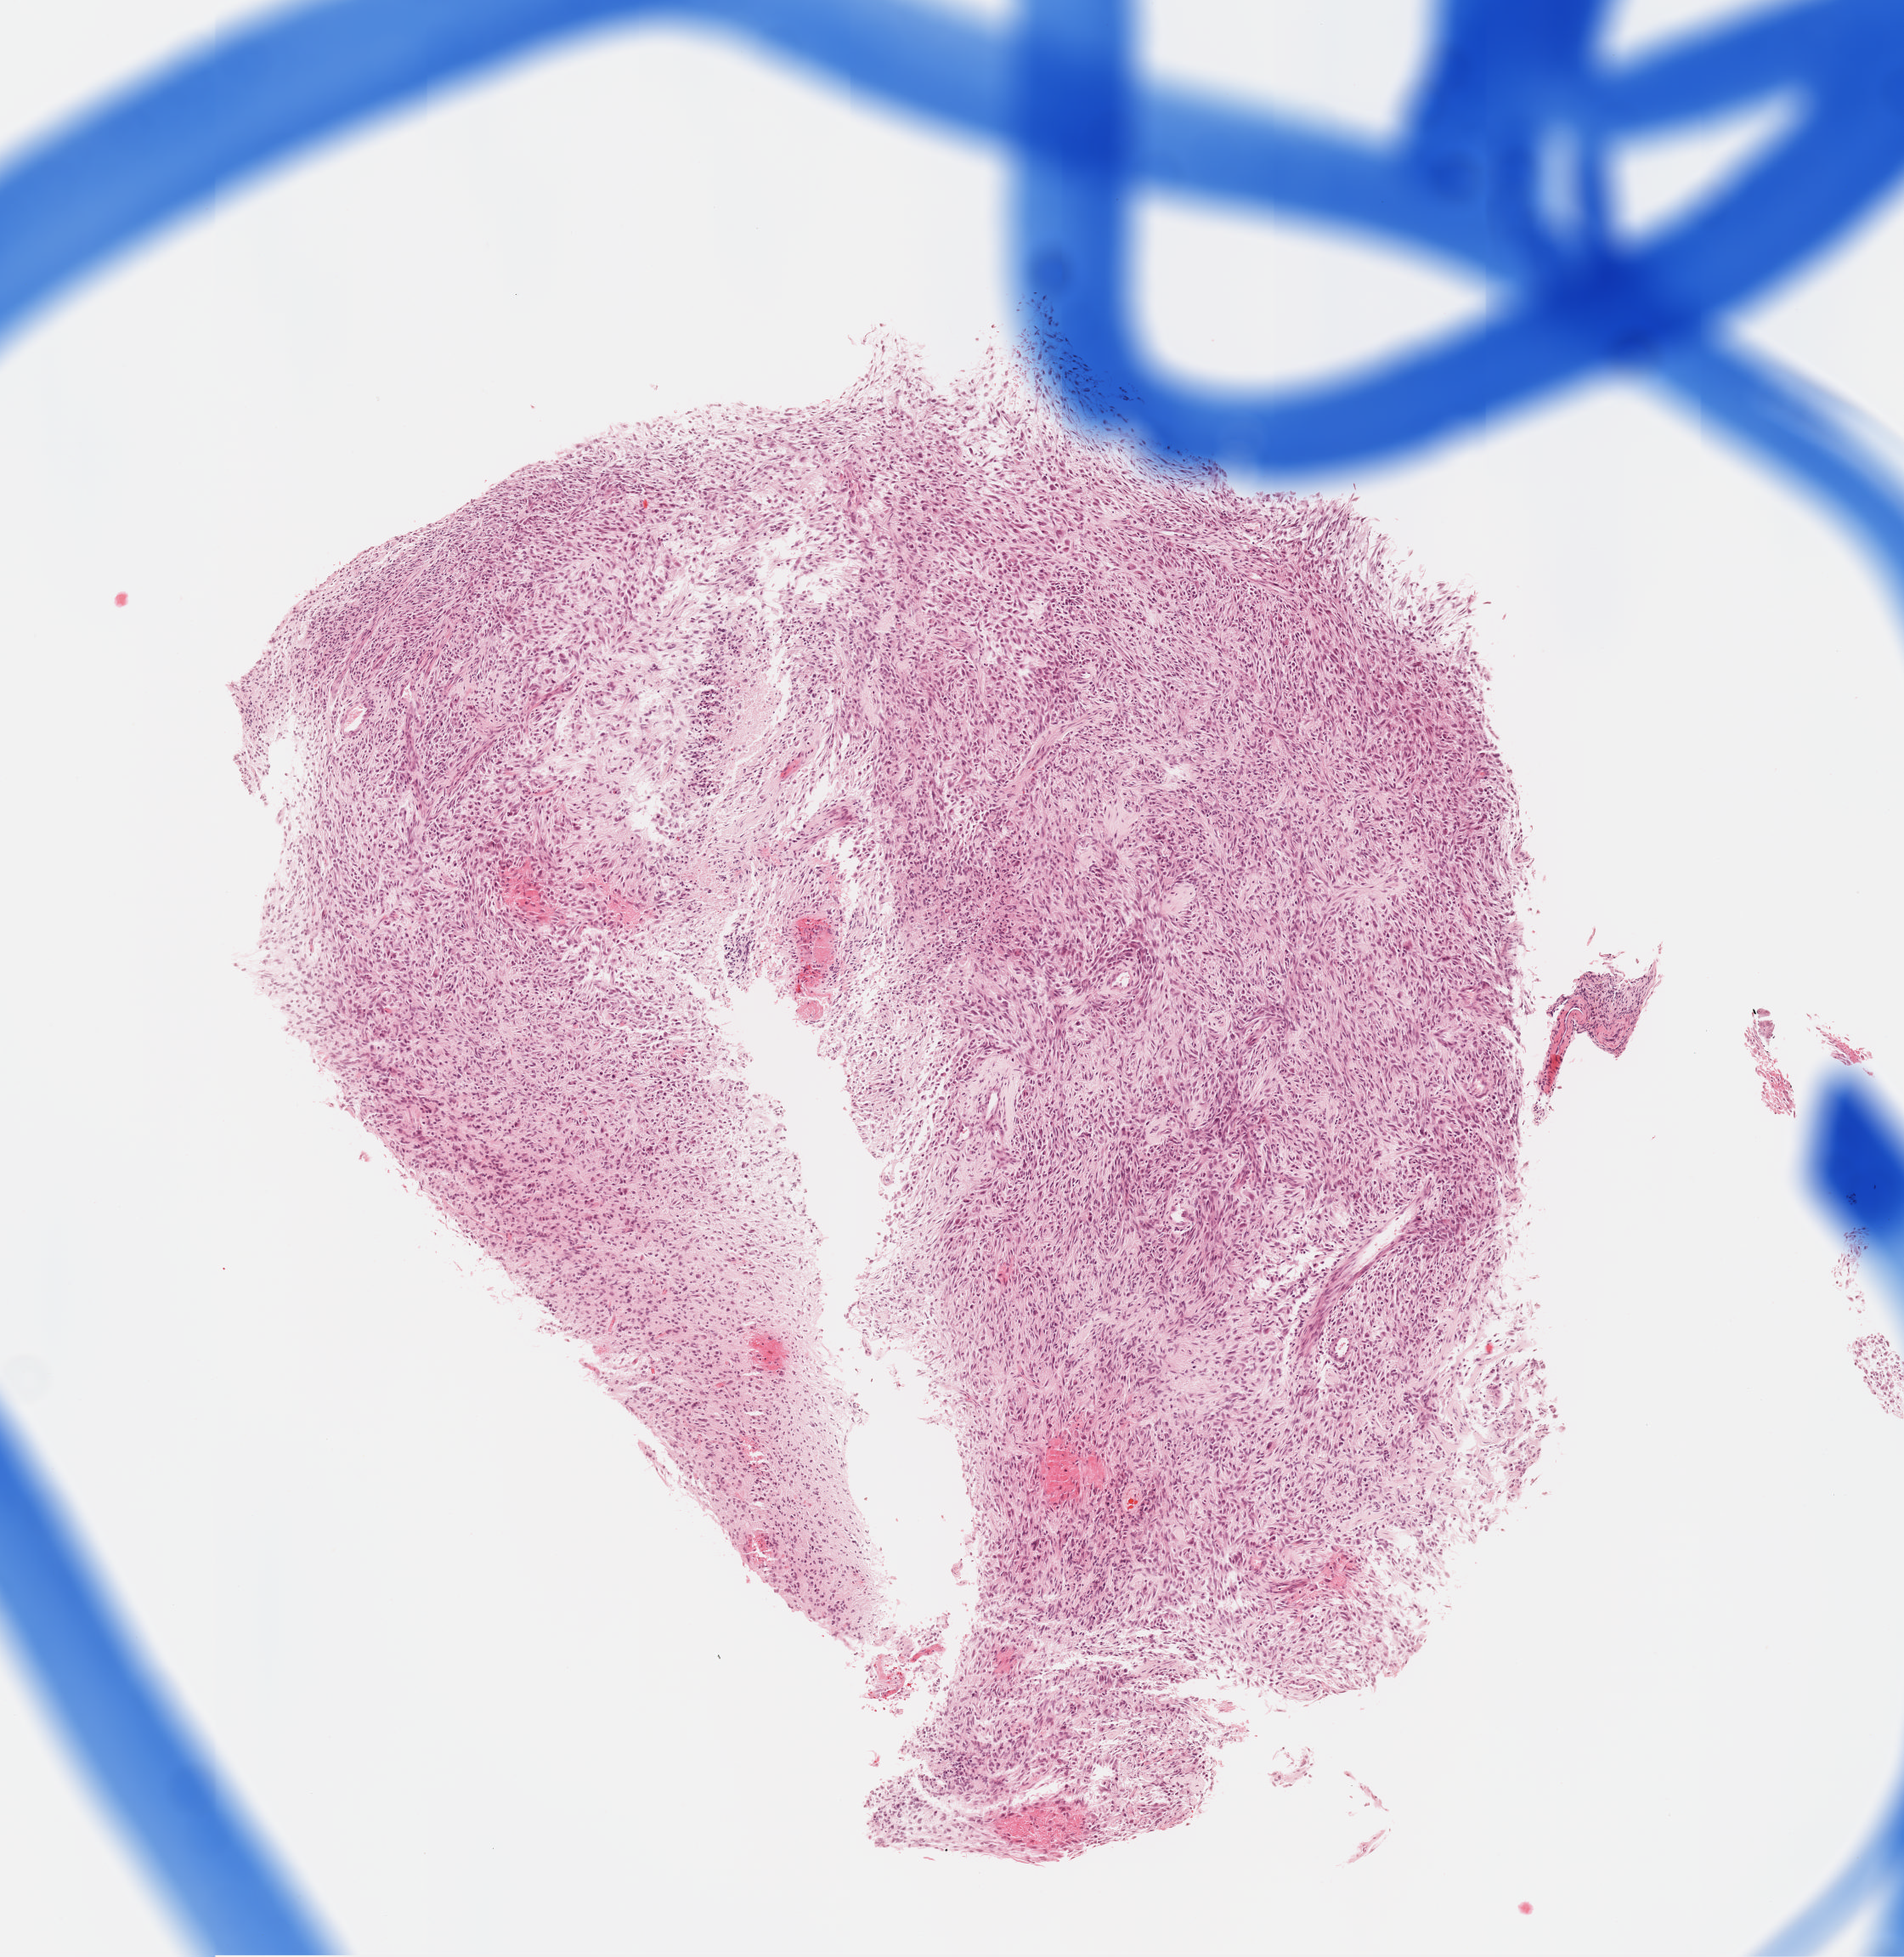
Digitized H&E-stained tissue section (whole slide), low-resolution overview of the scanned area, about 4.5 x 4.7 mm; formalin-fixed paraffin-embedded (FFPE) diagnostic section; sample: primary tumour, brain. Male, age 75 years at initial diagnosis.
Histologic diagnosis: Glioblastoma.